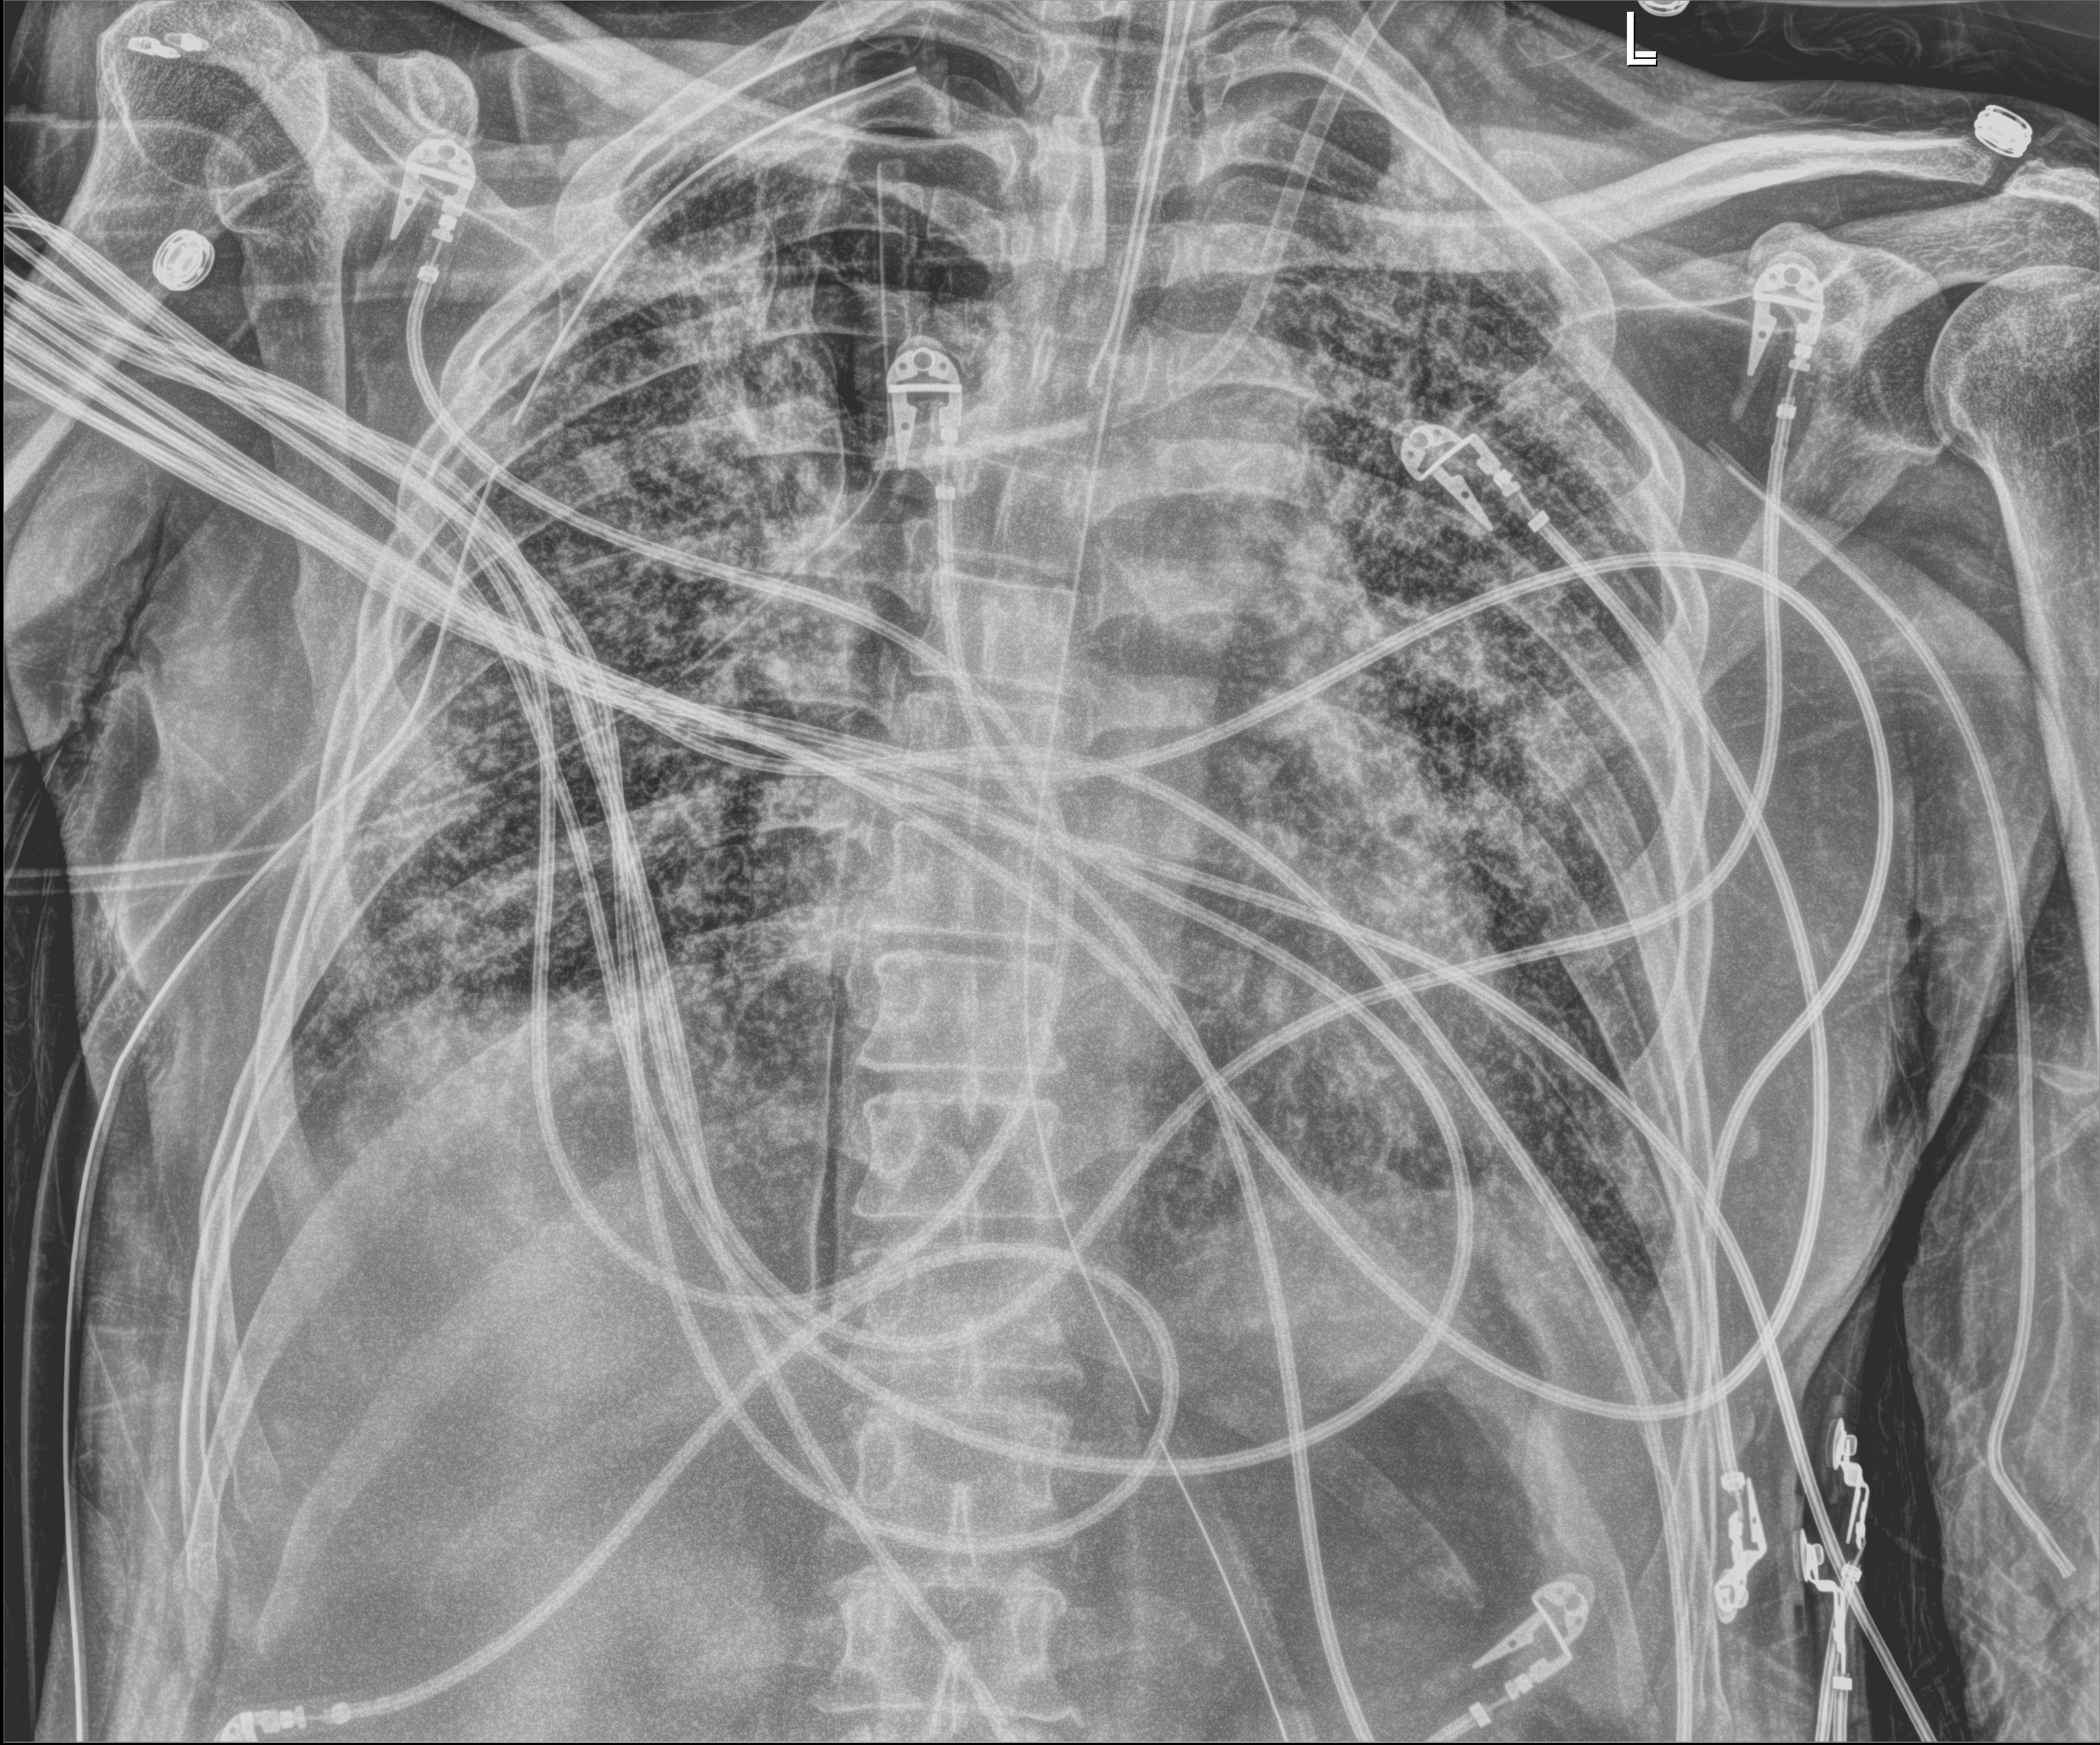
Portable chest radiograph, anteroposterior (AP) projection. Male patient hospitalised with COVID-19, age 60–74 years.
From the hospital-stay record, not from the radiograph (when in the stay this image was taken is not recorded):
- admitted to intensive care during this hospital stay: yes
- mechanically ventilated during this hospital stay: yes
- length of hospital stay: 65 days